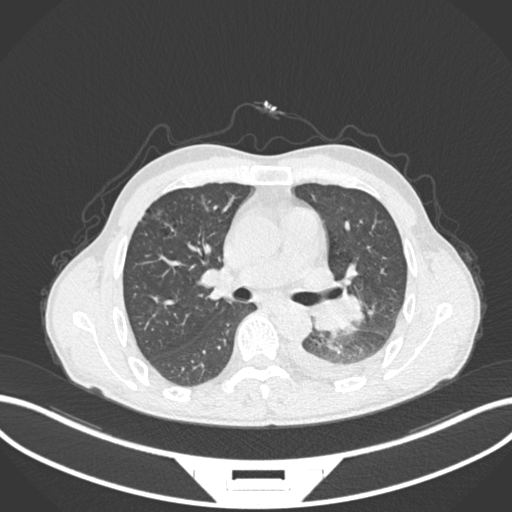
Chest CT, one axial slice; slice 146 of 222 in the series (ordered by position); reconstruction kernel B30f; 120 kVp; lung window (W 1500 / L -600 HU); 1 mm slice thickness; 512 × 512 image matrix. Patient: male, 47 years. Case-level facts recorded for this patient, not image findings: clinical TNM (as recorded): T3 N1 M1c.
Outlined on this slice (rectangle marked by the reading radiologist):
- lung tumour (recorded histology: small cell carcinoma): bounding box <305,294,363,334> (left, top, right, bottom; pixels)